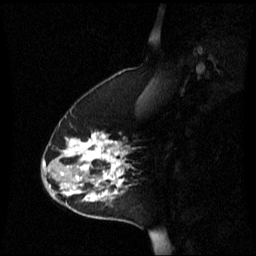
Breast MRI (dynamic contrast-enhanced), one sagittal slice. Slice 20 of 60 in the series (ordered by position). Dynamic contrast-enhanced series, image 2 of 3 at this slice position (ordered by acquisition). 1.5 T. TE 4.2 ms, TR 8.4 ms. 2.2 mm slice thickness. 256 × 256 image matrix. Patient: female, 45 years. From the clinical record (not read from this slice): setting: breast cancer imaged before/during neoadjuvant chemotherapy; receptor status: HR-positive, HER2-negative.
Outlined on this slice (semi-automatically segmented with operator editing):
- analysis volume of interest (the breast-tissue region the enhancement analysis was run in; not a lesion): bounding box (x1, y1, x2, y2) in pixels: (42, 132, 135, 221)
- tumour enhancement mask (voxels above the 70 % enhancement threshold inside the analysis volume of interest): (44, 132, 127, 203)